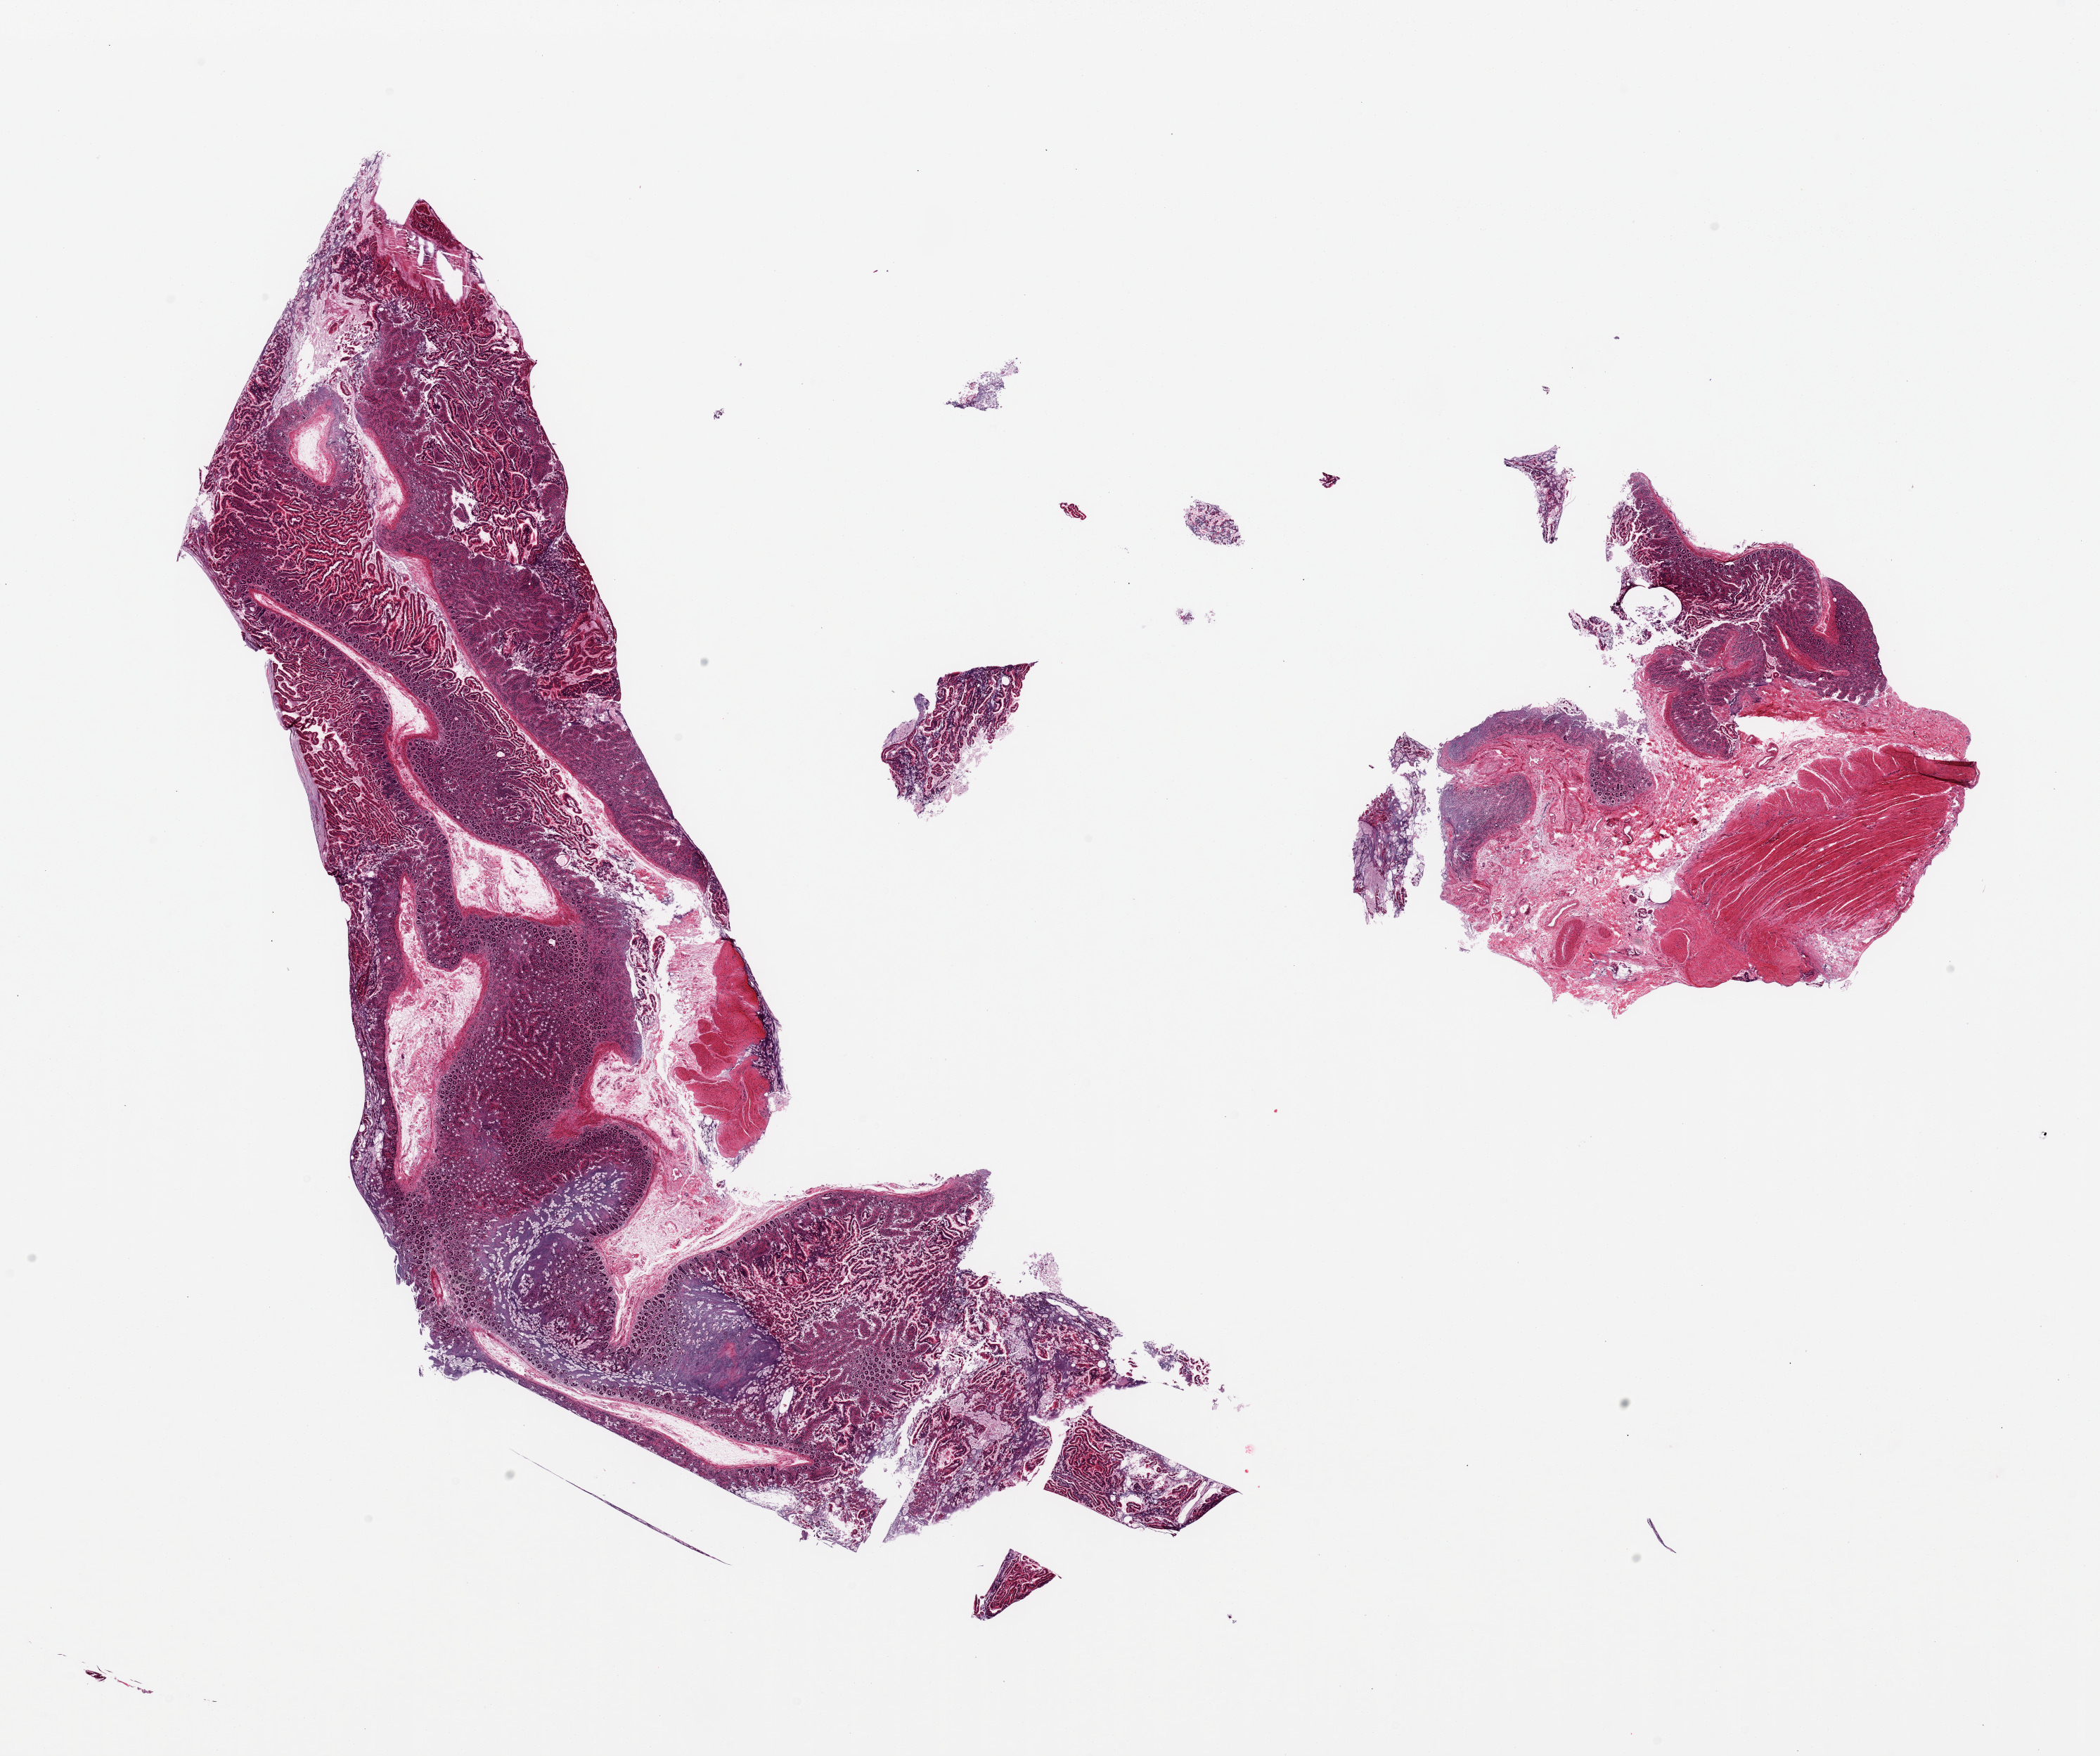
Hematoxylin and eosin (H&E) whole-slide image — whole scanned area (about 23.6 x 19.8 mm, slide scanned at 20x) shown as a low-resolution overview, PAXgene-fixed paraffin-embedded (PFPE) section, sampled site (target tissue): pancreas, donor tissue sample. Male donor.
Reviewer comment on this tissue sample: 2 pieces, crushed small bowel sections, not pancreas.